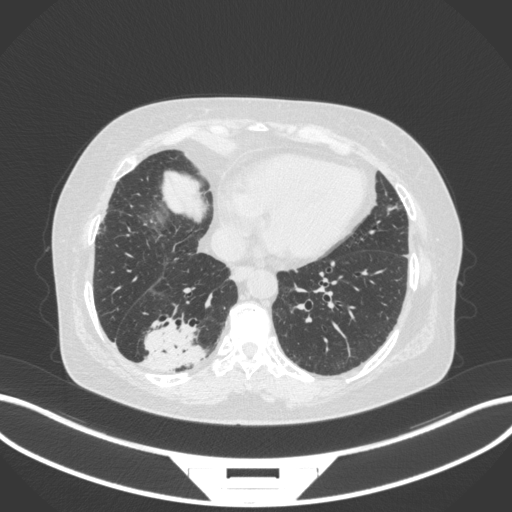
Chest CT, one axial slice; position 68 of 303 along the scan axis; 120 kVp; lung window (W 1500 / L -600 HU); 1 mm slice thickness; 512 × 512 image matrix, field of view 400 × 400 mm. Female patient, age 65 years. From the clinical record (not read from this slice): clinical TNM (as recorded): T2b N1 M0.
Outlined on this slice (rectangle marked by the reading radiologist):
- lung tumour (recorded histology: adenocarcinoma): bounding box (x1, y1, x2, y2) in pixels: (135, 316, 208, 373)